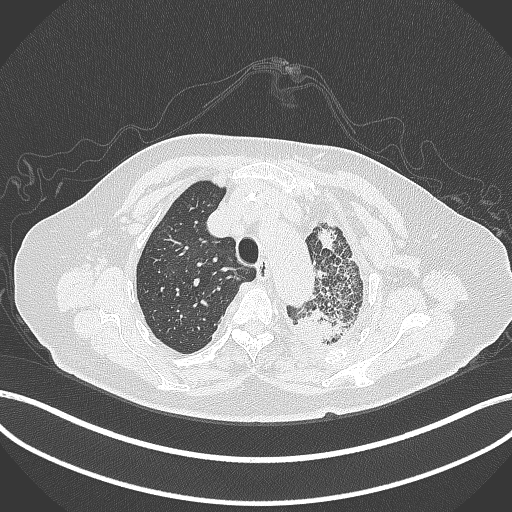
Chest CT, one axial slice. Position 312 of 399 along the scan axis. Reconstruction kernel B70f. 120 kVp. Lung window (W 1500 / L -600 HU). 512 × 512 image matrix. Patient: female, 75 years. Case-level facts recorded for this patient, not image findings: clinical TNM (as recorded): T3 N3 M1.
Outlined on this slice (bounding box drawn by a radiologist):
- lung tumour (recorded histology: adenocarcinoma): bounding box (x1, y1, x2, y2) in pixels: (291, 299, 356, 348)